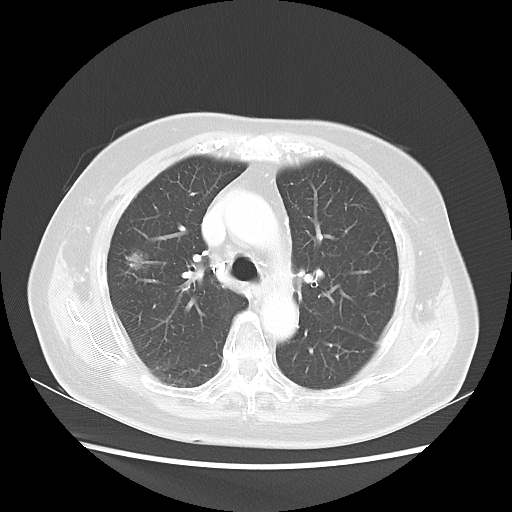
Chest CT, one axial slice. Slice 32 of 48 in the series (ordered by position). Reconstruction kernel LUNG. 100 kVp. Lung window (W 1500 / L -600 HU). 512 × 512 image matrix. Patient: female, 75 years. From the clinical record (not read from this slice): clinical TNM (as recorded): T1c N0 M0.
Structures marked on this image (bounding box drawn by a radiologist):
- lung tumour (recorded histology: adenocarcinoma): bounding box <125,250,149,280> (left, top, right, bottom; pixels)